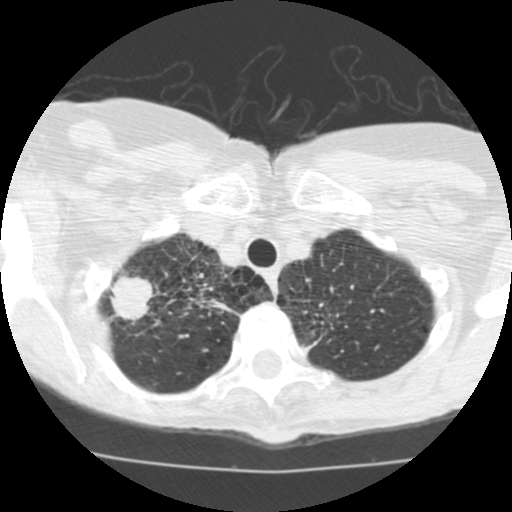
Low-dose screening chest CT, one axial slice. Position 101 of 115 along the scan axis. 120 kVp. Lung window (W 1500 / L -600 HU). 2.5 mm slice thickness. 512 × 512 image matrix, field of view 280 × 280 mm.
Structures marked on this image (expert manual segmentation):
- lesion 1 (tumor, upper lobe of right lung): bounding box [x1, y1, x2, y2] px = [109, 272, 154, 322]